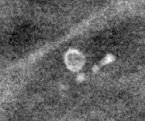
Crop from a digitized film mammogram around one marked abnormality, right breast, MLO view.
Marked abnormality: calcifications, morphology skin, distribution regional; BI-RADS assessment category 2; benign without callback (not worked up further).